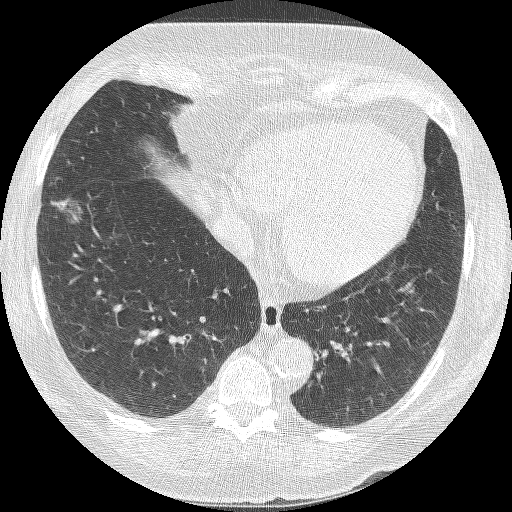
Axial slice from a low-dose chest CT screening exam; second annual screen; lung window (W 1500 / L -600 HU); 1.25 mm slice thickness; lung (sharp) reconstruction kernel (BONE); slice 93 of 245 in the series; 512 × 512 image matrix, field of view 310 × 310 mm. Female participant, aged 68 years at enrolment. Current smoker at enrolment.
Expert-annotated lung lesion, box from (x=34, y=192) to (x=86, y=246) px. Reader record for this screening exam (exam-level; its link to the box is not recorded): non-calcified nodule or mass ≥4 mm, right lower lobe, 18 × 15 mm, poorly defined margins, ground glass attenuation, pre-existing on the prior screen: yes; interval growth: yes. Official screen result: positive, other.